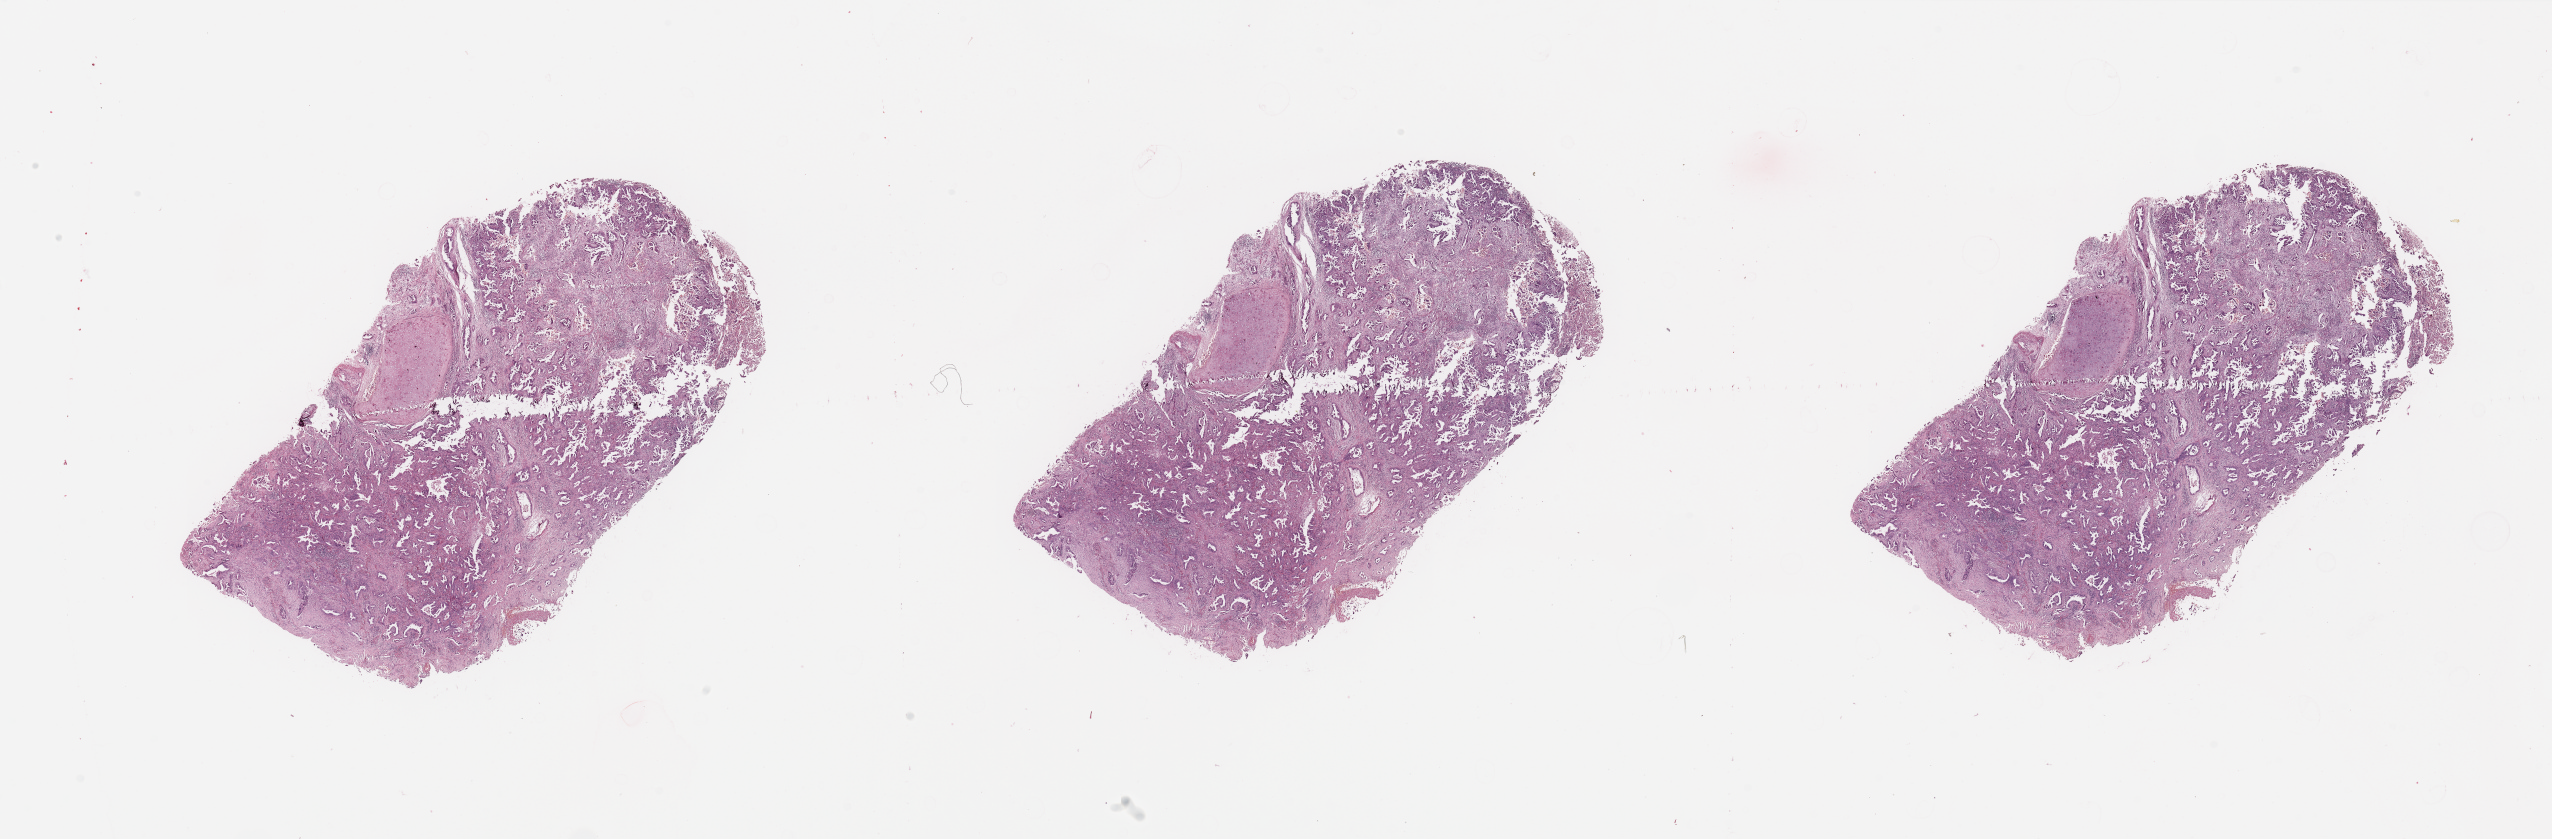
Digitized H&E-stained tissue section (whole slide) — shown as a low-resolution overview of the whole scanned area (about 40.4 x 13.3 mm); lung, tumour tissue. Female, 73 y/o. Histologic grade: G2 (moderately differentiated).
AJCC pathologic stage: IIIA. Diagnosis: Adenocarcinoma, NOS.